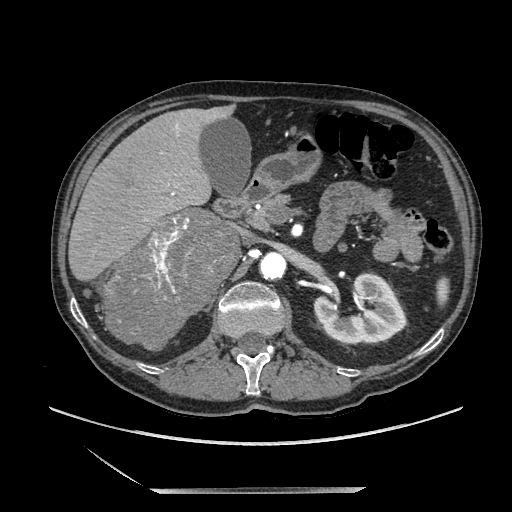
Contrast-enhanced abdominal CT, one axial slice; slice 112 of 243 in the series (ordered by position); soft-tissue window (W 400 / L 40 HU); 1.25 mm slice thickness; 512 × 512 image matrix. Male patient. Case-level facts recorded for this patient, not image findings: diagnosis: adrenocortical carcinoma; tumour side: right adrenal; tumour size at pathology: 16 cm; Ki-67 index: 17 %; stage (as recorded): 3.
Outlined on this slice (semi-automatically segmented with operator editing):
- mass: bounding box [x1, y1, x2, y2] px = [109, 210, 239, 349]